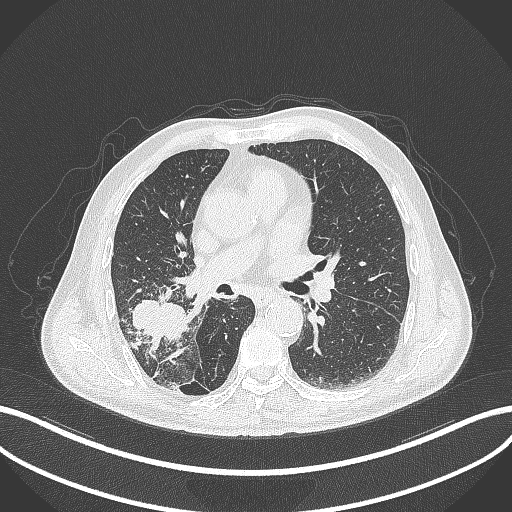
Chest CT, one axial slice; position 228 of 429 along the scan axis; reconstruction kernel B70f; 120 kVp; lung window (W 1500 / L -600 HU); 512 × 512 image matrix, field of view 400 × 400 mm. Patient: male, 72 years. From the clinical record (not read from this slice): clinical TNM (as recorded): T3 N2 M0.
Outlined on this slice (rectangle marked by the reading radiologist):
- lung tumour (recorded histology: adenocarcinoma): box from (x=125, y=295) to (x=191, y=346) px